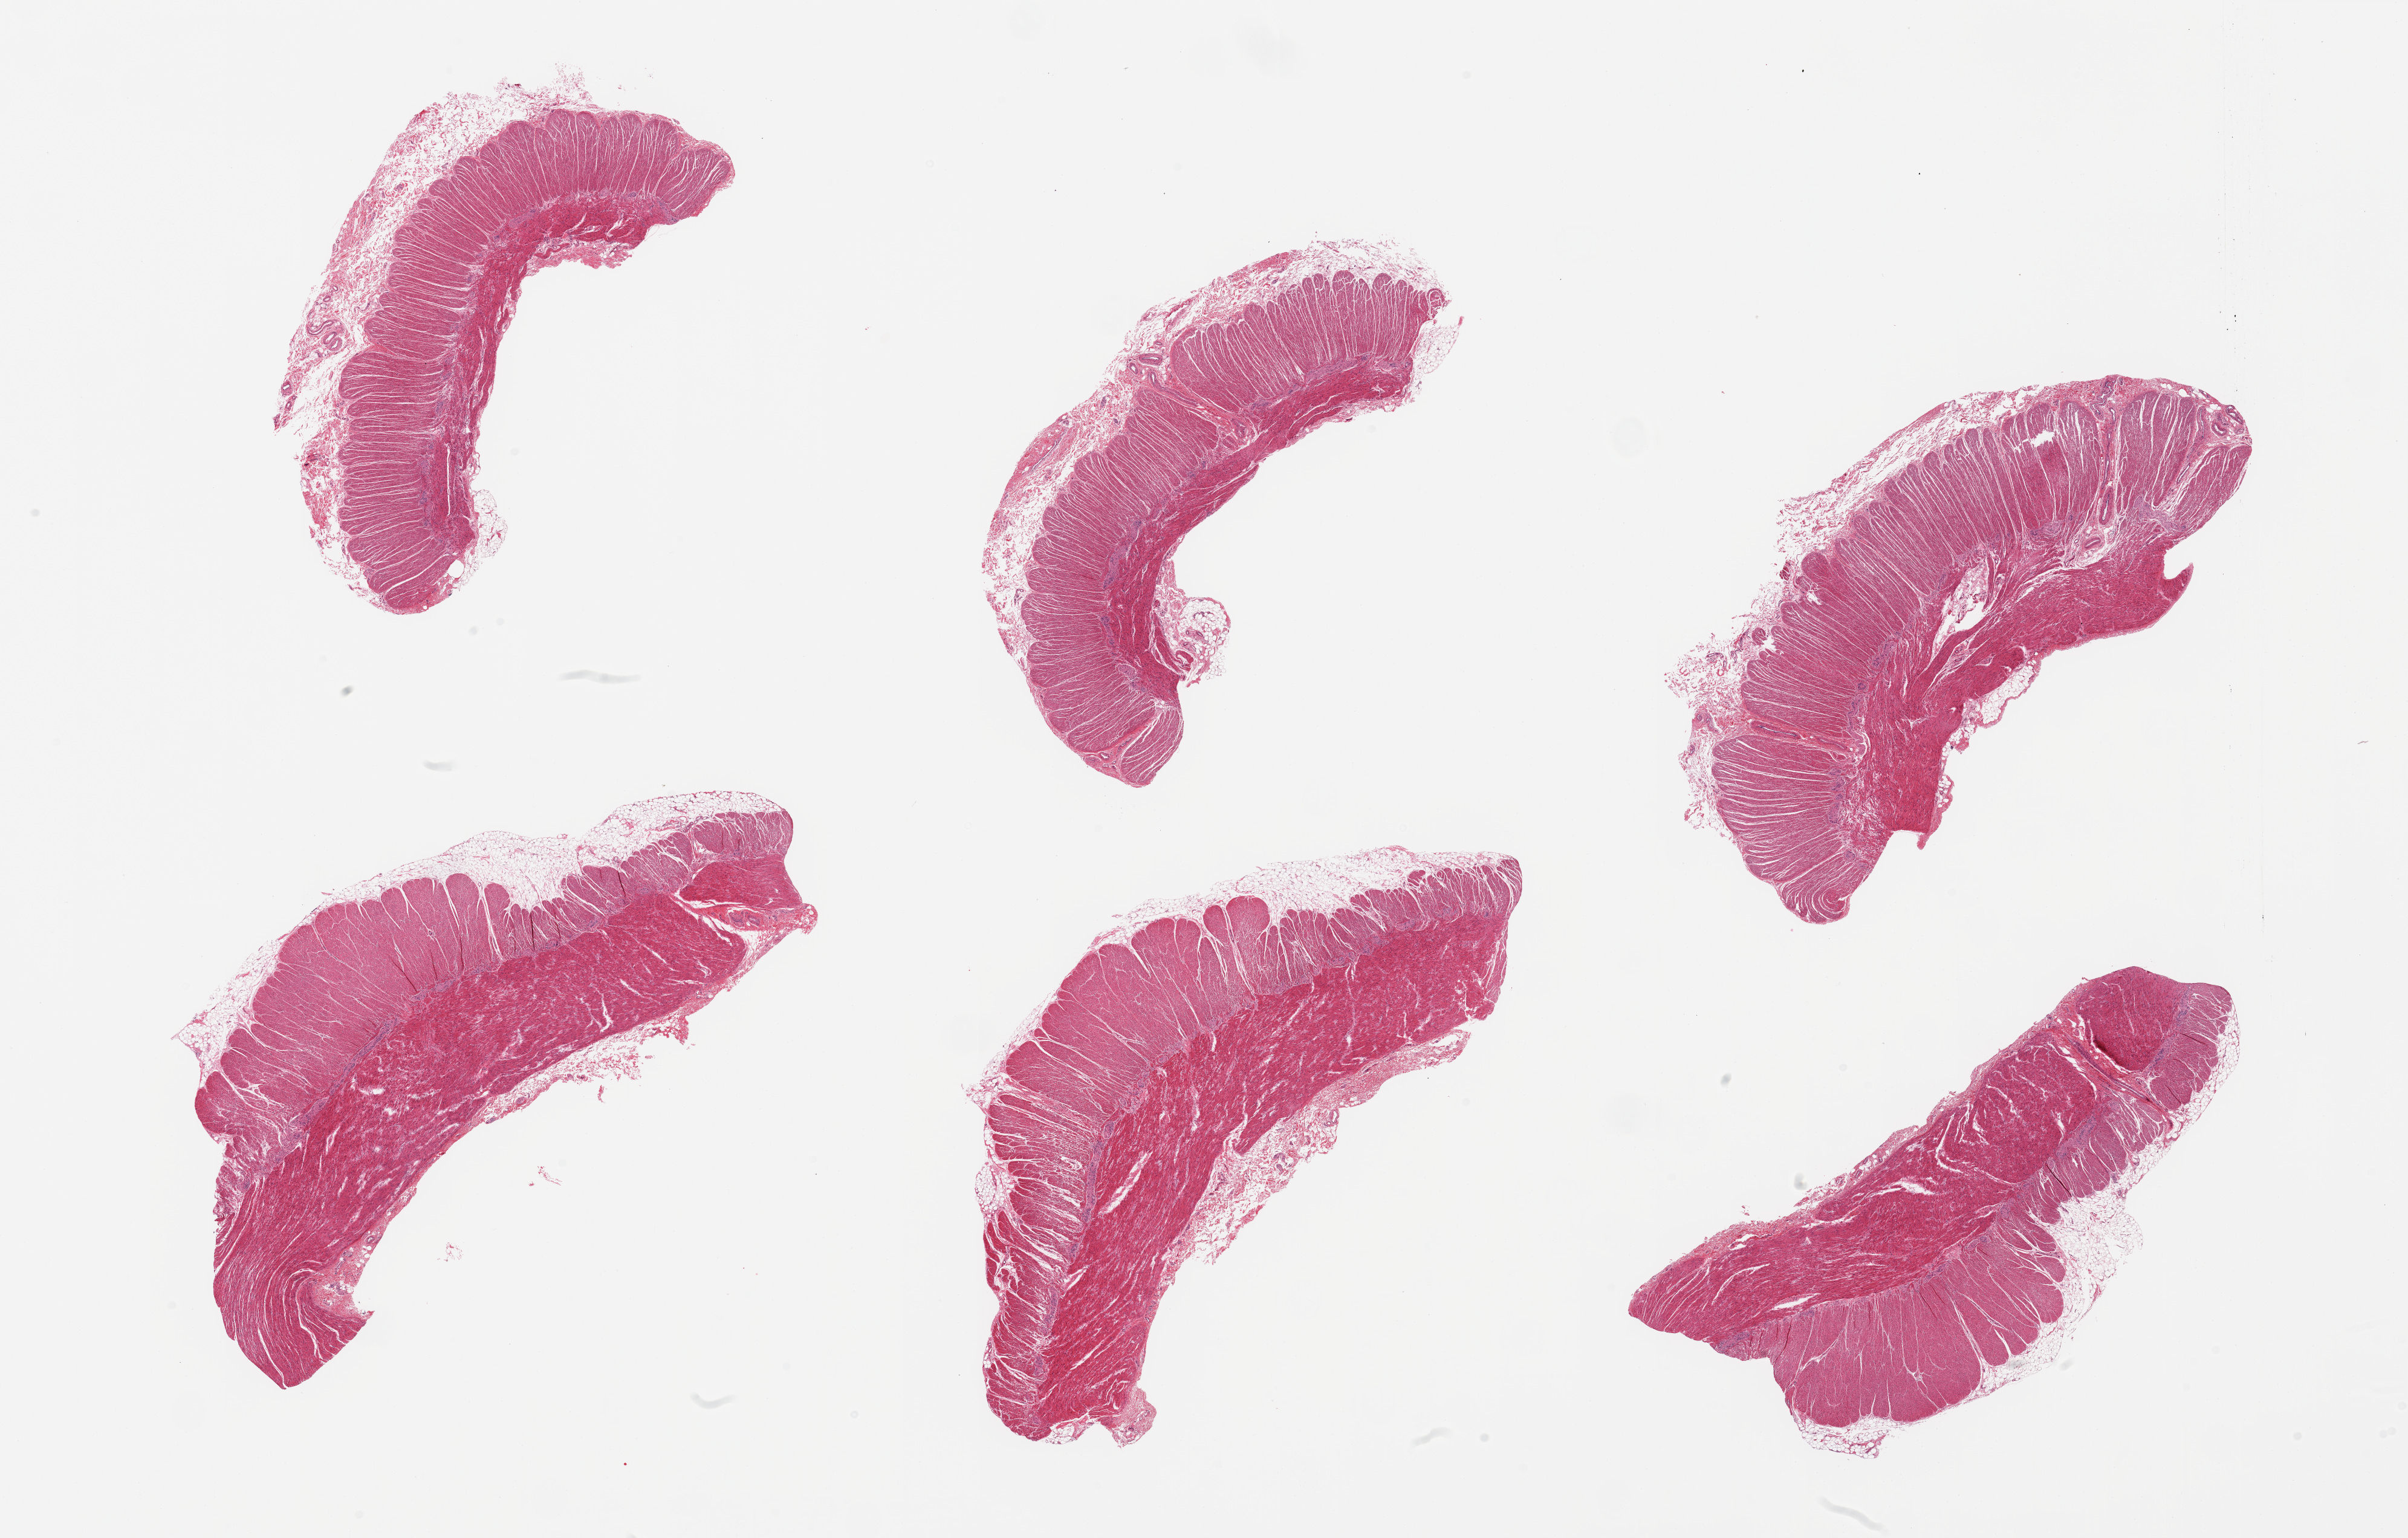
Whole-slide image, hematoxylin and eosin (H&E) stain — whole scanned area (about 31.5 x 20.1 mm) shown as a low-resolution overview. PAXgene-fixed, paraffin-embedded tissue. Target tissue: sigmoid colon. Tissue donor sample. Female donor.
• review note (as recorded): 6 pieces, adherent fat/serosa on several sections up to ~0.7mm